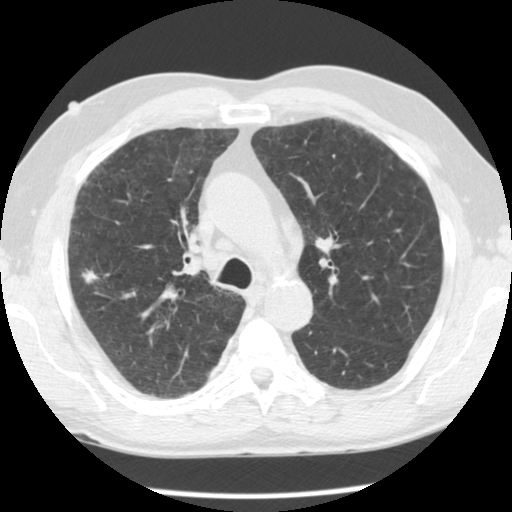
Low-dose screening chest CT, one axial slice; reconstruction kernel STANDARD; lung window (W 1500 / L -600 HU); 2.5 mm slice thickness; 512 × 512 image matrix, field of view 330 × 330 mm.
Structures marked on this image (expert manual segmentation):
- lesion 2 (nodule): bounding box <82,269,99,284> (left, top, right, bottom; pixels)